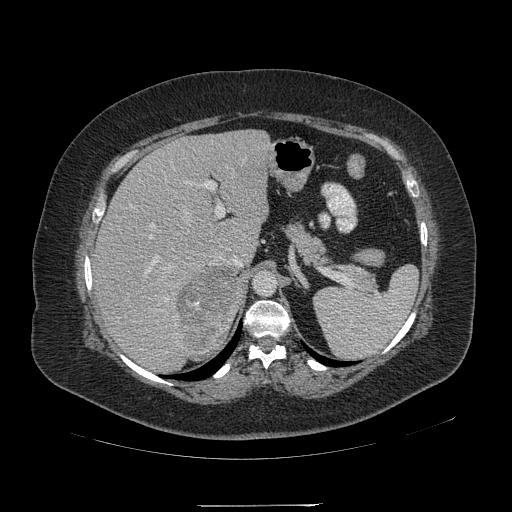
Contrast-enhanced abdominal CT, one axial slice. Slice 147 of 217 in the series (ordered by position). Reconstruction kernel STANDARD. Intravenous contrast given. Soft-tissue window (W 400 / L 40 HU). 1.25 mm slice thickness. 512 × 512 image matrix, field of view 453 × 453 mm. Female patient, age 55 years. From the clinical record (not read from this slice): diagnosis: adrenocortical carcinoma; tumour side: right adrenal; tumour size at pathology: 11 cm; Ki-67 index: 20 %; stage (as recorded): 2.
Structures marked on this image (semi-automatic segmentation, software-assisted and operator-edited):
- mass: bounding box <179,267,241,360> (left, top, right, bottom; pixels)